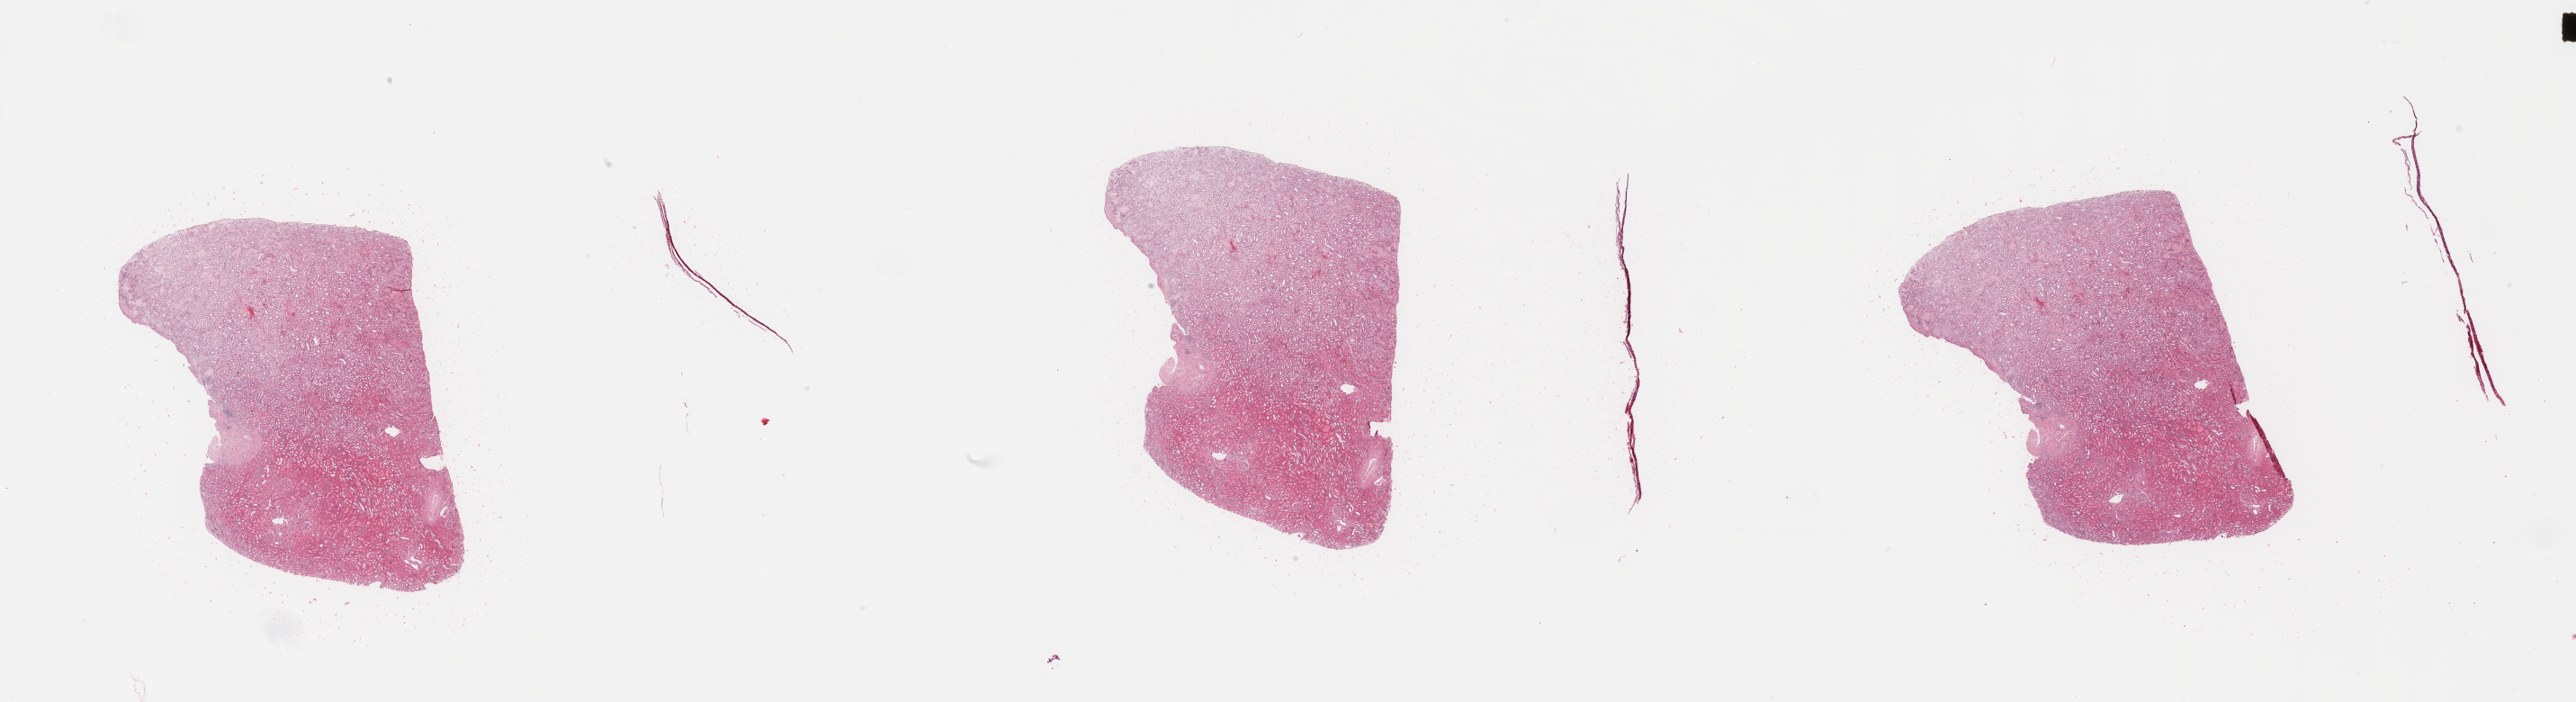
Digitized H&E tissue section (whole slide), whole scanned area (about 45.3 x 12.3 mm, from a 20x scan) shown as a low-resolution overview. Normal (non-tumour) tissue sample, sampled site: kidney. 62-year-old male patient.
This section: normal (non-tumour) tissue from the same patient. Patient diagnosis: Renal cell carcinoma, NOS.